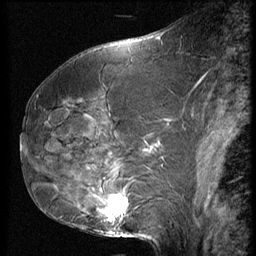
Breast MRI (dynamic contrast-enhanced), one sagittal slice; slice 29 of 62 in the series (ordered by position); 3 images stored at this slice position (order not interpretable as contrast timing); 1.5 T; TE 4.2 ms, TR 9 ms; 256 × 256 image matrix. Patient: female, 50 years. Case-level facts recorded for this patient, not image findings: setting: breast cancer imaged before/during neoadjuvant chemotherapy; receptor status: HR-positive, HER2-negative.
Outlined on this slice (semi-automatically segmented with operator editing):
- analysis volume of interest (the breast-tissue region the enhancement analysis was run in; not a lesion): bounding box <59,125,139,238> (left, top, right, bottom; pixels)
- tumour enhancement mask (voxels above the 140 % enhancement threshold inside the analysis volume of interest): <105,194,129,221>